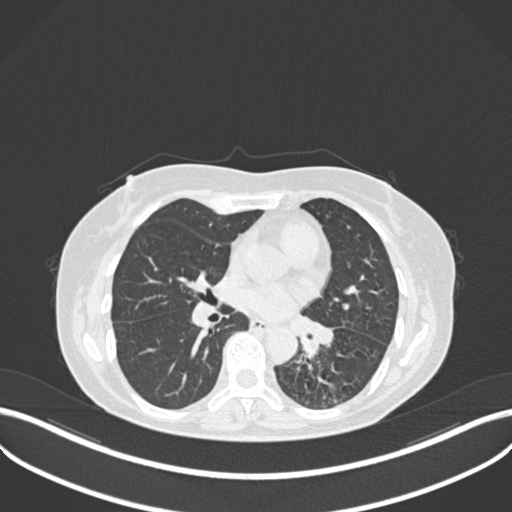
Chest CT, one axial slice; slice 129 of 270 in the series (ordered by position); reconstruction kernel B30f; 120 kVp; lung window (W 1500 / L -600 HU); 1 mm slice thickness; 512 × 512 image matrix. Patient: female, 63 years. From the clinical record (not read from this slice): clinical TNM (as recorded): T1b N0 M0; histopathological grade: G2-3.
Outlined on this slice (bounding box drawn by a radiologist):
- lung tumour (recorded histology: adenocarcinoma): box from (x=286, y=307) to (x=337, y=364) px